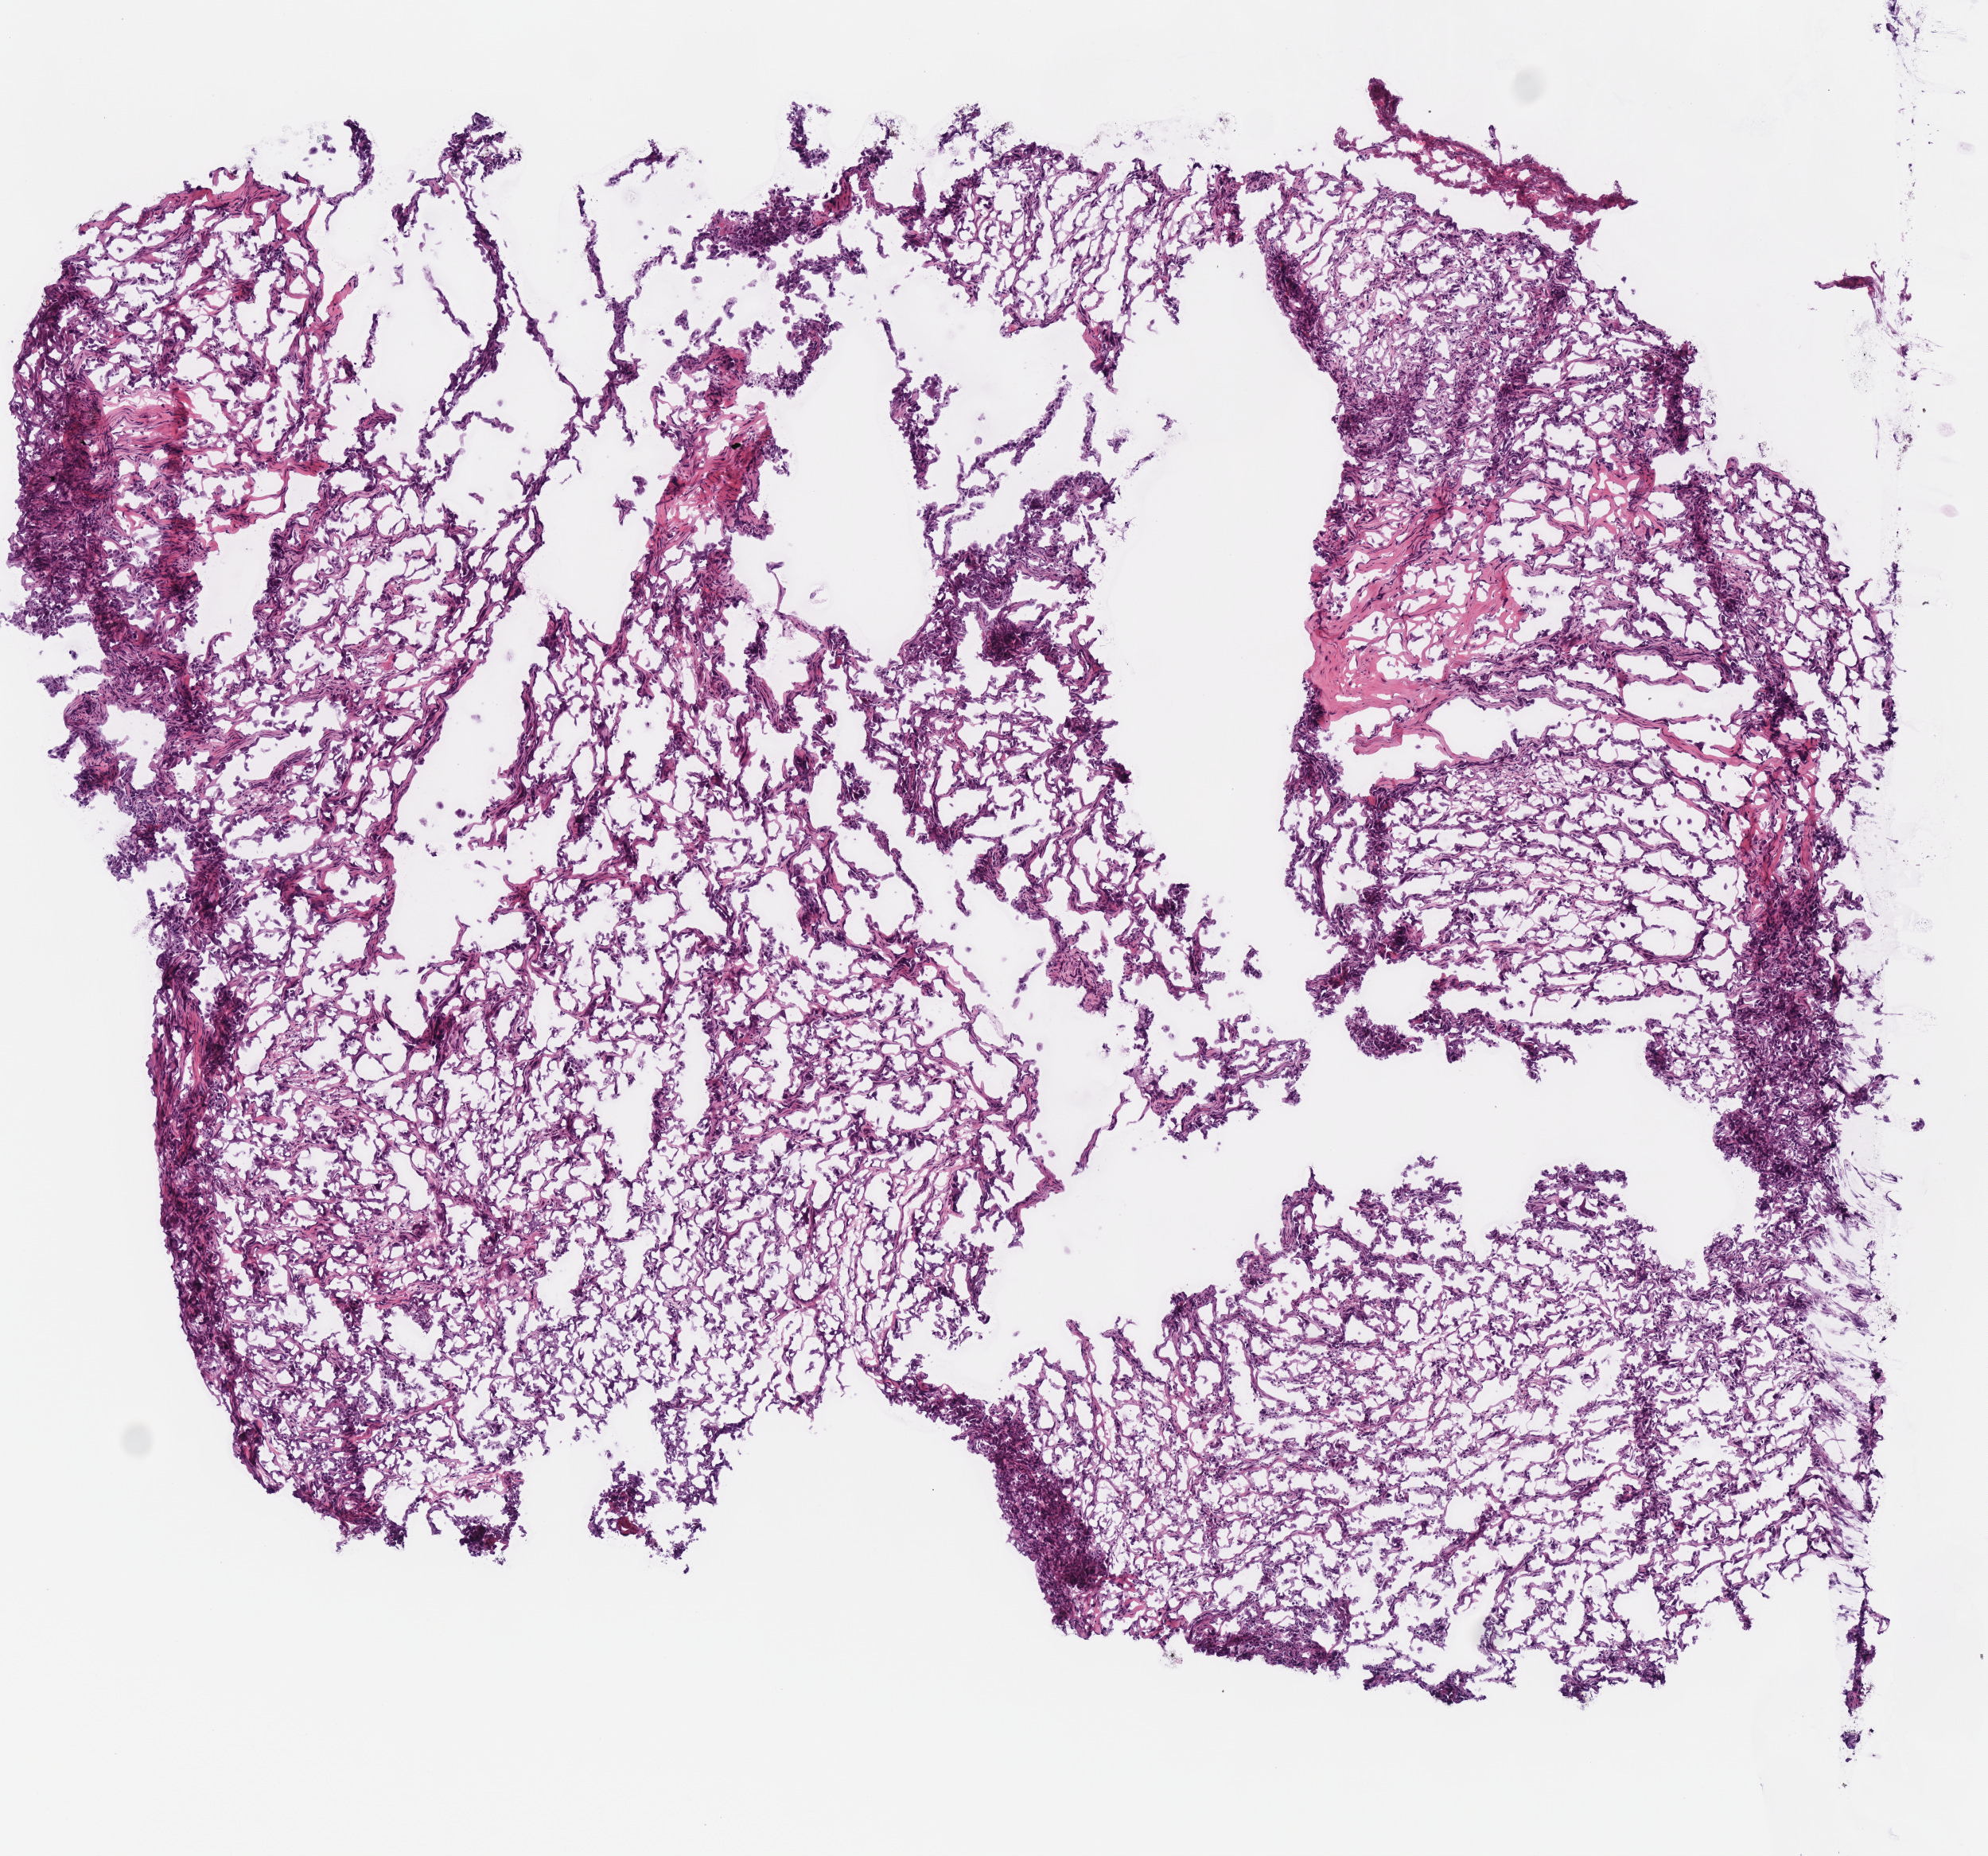
Whole-slide histology image, H&E-stained — shown as a low-resolution overview of the whole scanned area (about 4.9 x 4.6 mm). Frozen section from the bottom of the tissue portion. Sample: primary tumour, head and neck. Patient: male, age at initial diagnosis 55 years. Histologic grade: G3 (poorly differentiated). Slide review estimates, as recorded: tumour cells 100%, tumour nuclei 51%, normal cells 0%, stromal cells 0%, necrosis 0%. Inflammatory infiltration, as recorded: lymphocyte infiltration 10%, monocyte infiltration 0%, neutrophil infiltration 0%.
• AJCC pathologic stage: IVA (7th edition)
• lymph nodes positive (case pathology): 14 of 24 examined
• histologic diagnosis: Squamous cell carcinoma, NOS (overlapping lesion of lip, oral cavity and pharynx)
• laterality: right